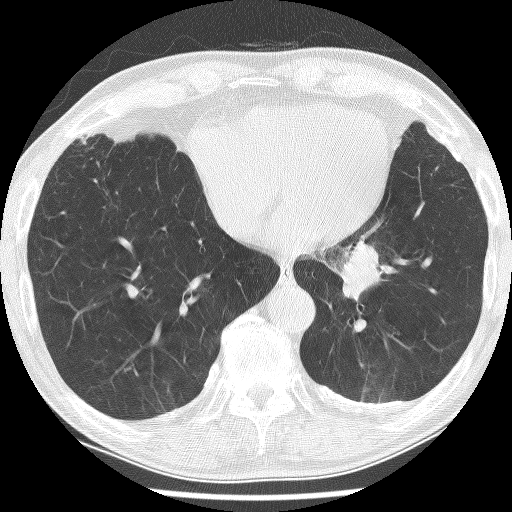
Axial slice from a low-dose chest CT screening exam; first (baseline) screen; lung window (W 1500 / L -600 HU); 2.5 mm slice thickness; 120 kVp; 512 × 512 image matrix, field of view 320 × 320 mm. Male, age 74 years at enrolment. Current smoker at enrolment.
• Expert-annotated lung lesion, bounding box (x1, y1, x2, y2) in pixels: (317, 227, 423, 320).
• Reader record for this screening exam (exam-level; its link to the box is not recorded): non-calcified nodule or mass ≥4 mm, left lower lobe, 30 × 27 mm, spiculated (stellate) margins, soft tissue attenuation.
• Later outcome: lung cancer diagnosed 151 days after this screen — adenocarcinoma, NOS, left lower lobe, stage IIIA (AJCC 6th edition), 49 mm at pathology.